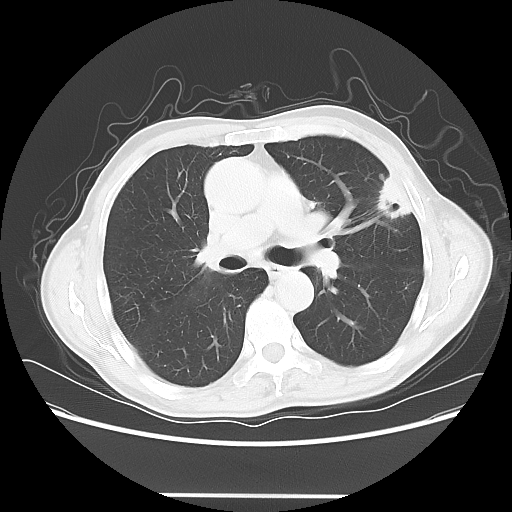
Chest CT, one axial slice; slice 38 of 64 in the series (ordered by position); reconstruction kernel LUNG; 120 kVp; lung window (W 1500 / L -600 HU); 5 mm slice thickness; 512 × 512 image matrix. Male patient, age 71 years. Case-level facts recorded for this patient, not image findings: clinical TNM (as recorded): T1c N0 M0.
Structures marked on this image (bounding box drawn by a radiologist):
- lung tumour (recorded histology: adenocarcinoma): bounding box (x1, y1, x2, y2) in pixels: (374, 171, 415, 228)